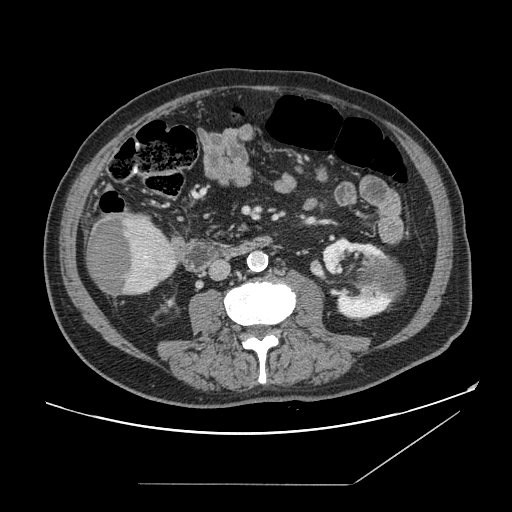
Contrast-enhanced abdominal CT, one axial slice. Slice 39 of 166 in the series (ordered by position). Intravenous contrast given. Soft-tissue window (W 400 / L 40 HU). 2.5 mm slice thickness. 512 × 512 image matrix, field of view 416 × 416 mm. Male patient, age 80 years. Case-level facts recorded for this patient, not image findings: diagnosis: colorectal cancer liver metastases, imaged before liver resection; multiple liver metastases: no; largest metastasis: 2.2 cm; disease in both lobes: no.
Outlined on this slice (manually delineated by an expert):
- liver: bounding box <88,212,177,295> (left, top, right, bottom; pixels)
- liver metastasis: <90,218,134,293>